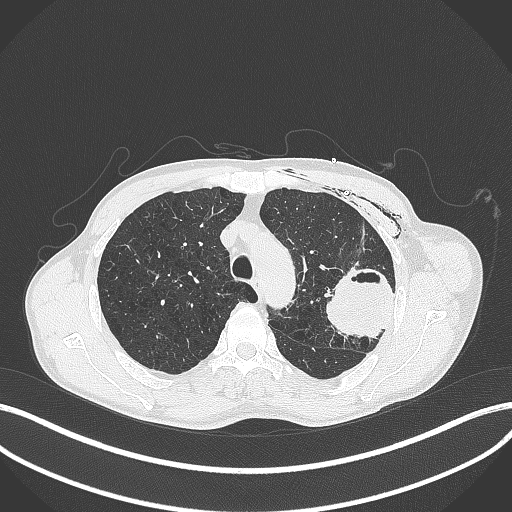
Chest CT, one axial slice; reconstruction kernel B70f; lung window (W 1500 / L -600 HU); 1 mm slice thickness; 512 × 512 image matrix, field of view 400 × 400 mm. Male patient, age 58 years. Case-level facts recorded for this patient, not image findings: clinical TNM (as recorded): T3 N0 M0.
Annotated regions visible in this slice (bounding box drawn by a radiologist):
- lung tumour (recorded histology: adenocarcinoma): bounding box (x1, y1, x2, y2) in pixels: (324, 267, 398, 343)